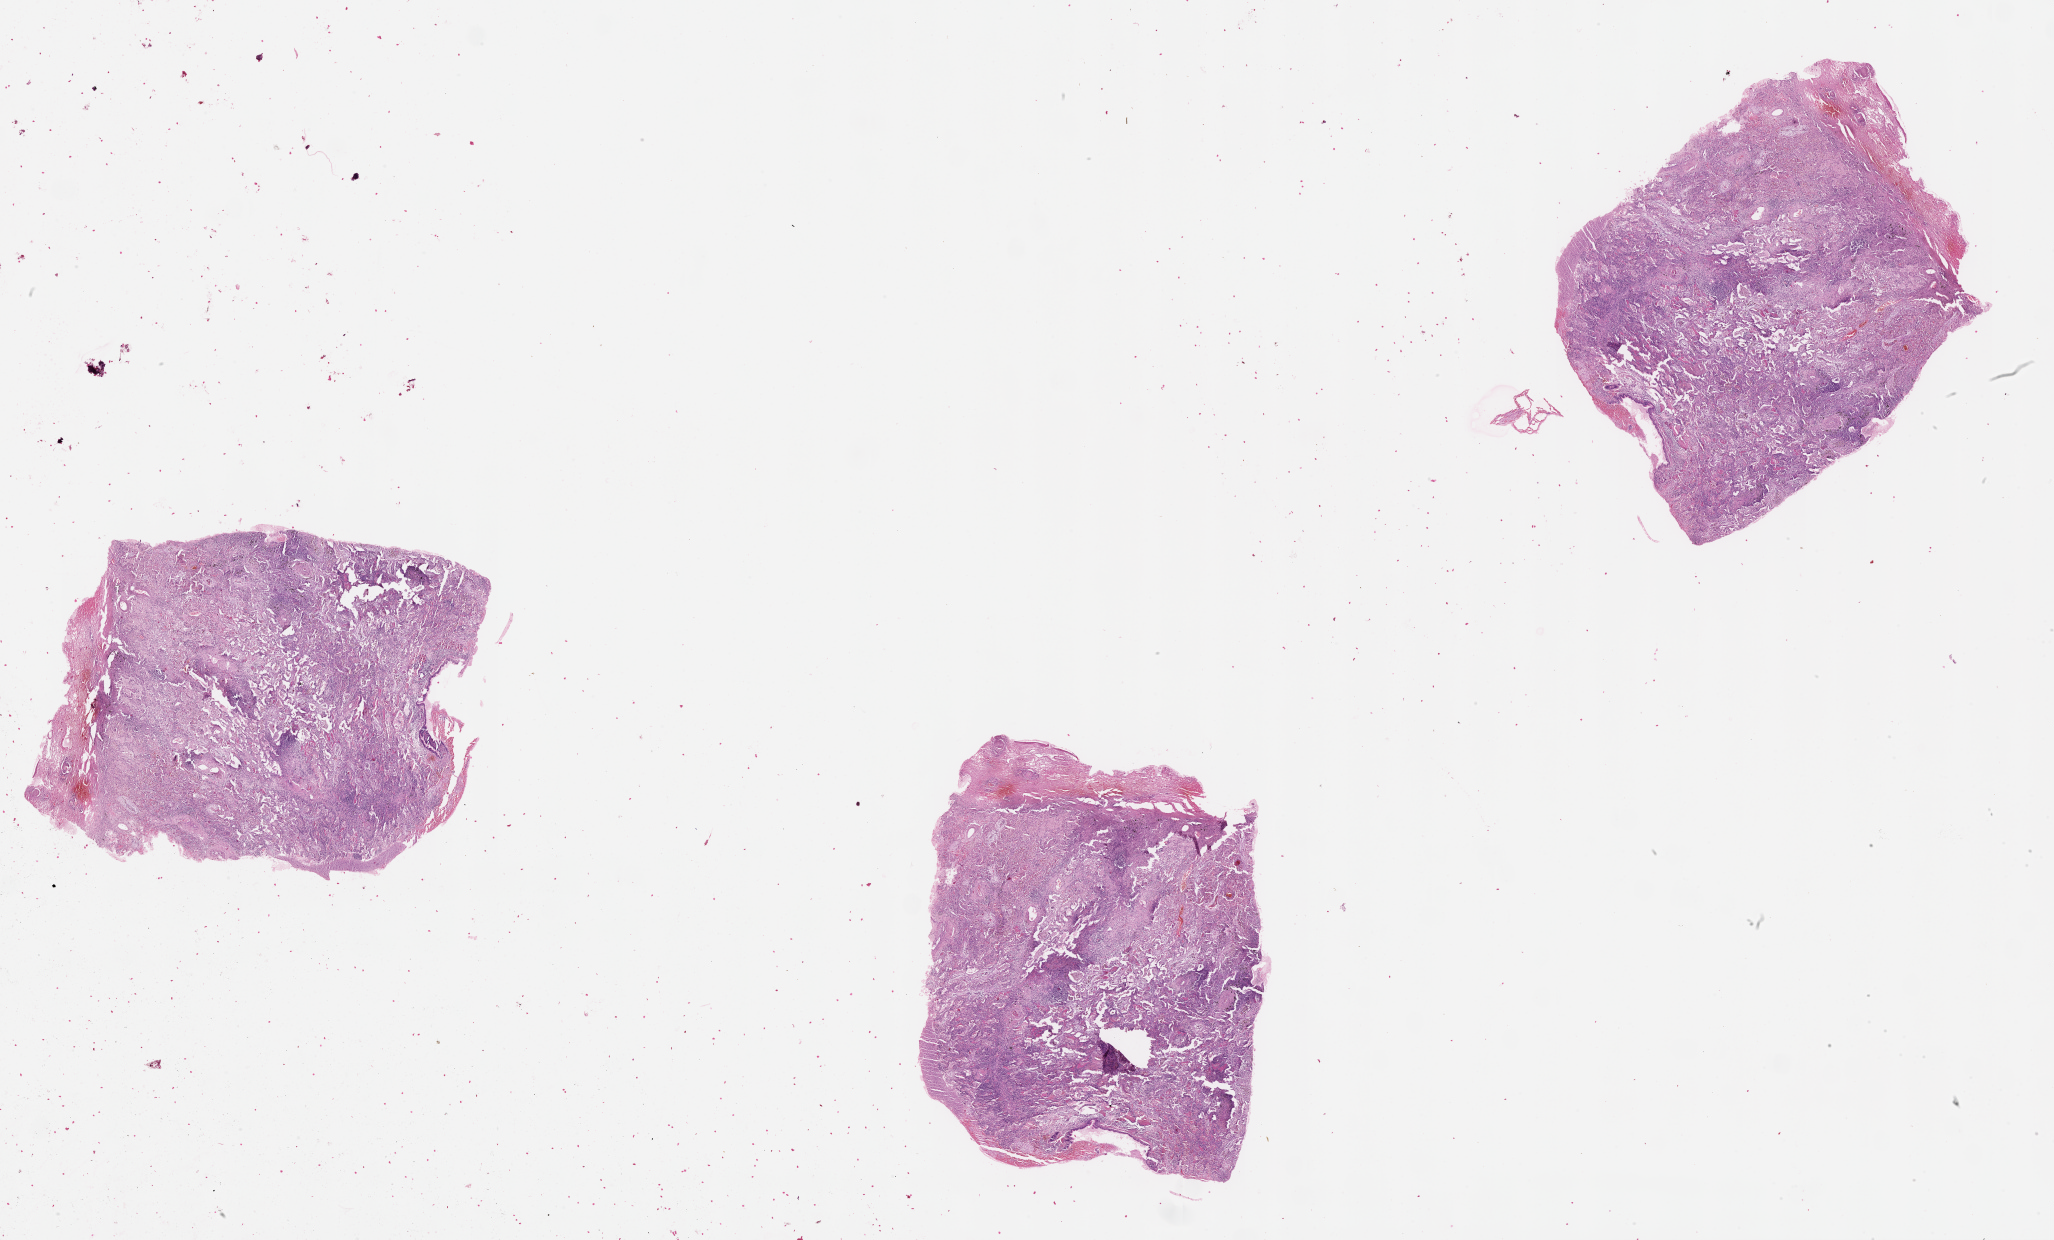
Whole-slide histology image, H&E, low-resolution overview of the scanned area, about 33.1 x 20.0 mm (from a 20x scan). Lung, normal (non-tumour) tissue. Male, 59 y/o.
• this section: normal (non-tumour) tissue from the same patient
• patient diagnosis (cohort enrolment): squamous cell carcinoma (lung)